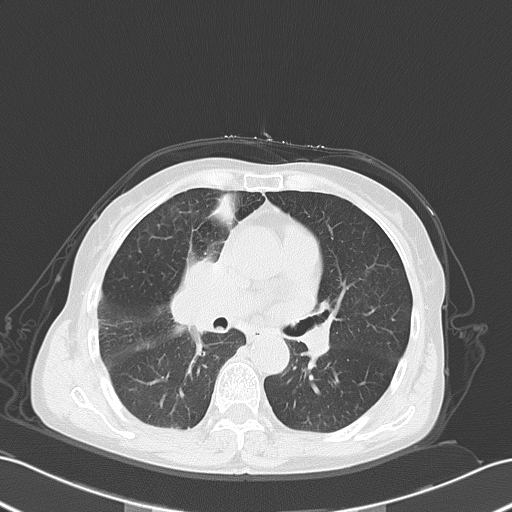
Chest CT, one axial slice. Slice 30 of 55 in the series (ordered by position). Reconstruction kernel B70f. 120 kVp. Lung window (W 1500 / L -600 HU). 5 mm slice thickness. 512 × 512 image matrix, field of view 353 × 353 mm. Female patient, age 67 years. From the clinical record (not read from this slice): clinical TNM (as recorded): T2a N3 M0.
Outlined on this slice (bounding box drawn by a radiologist):
- lung tumour (recorded histology: small cell carcinoma): bounding box (x1, y1, x2, y2) in pixels: (169, 256, 231, 336)